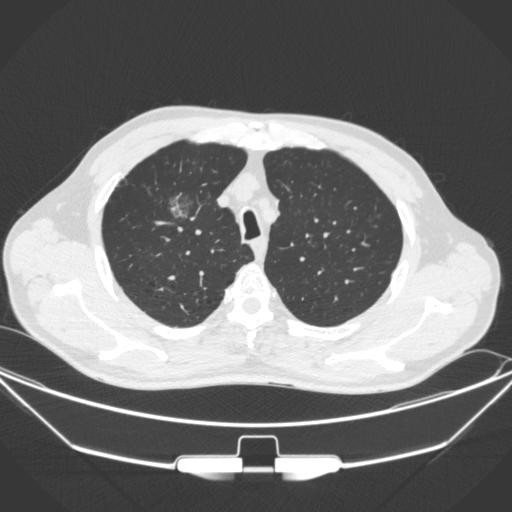
Chest CT, one axial slice. Position 272 of 355 along the scan axis. Lung window (W 1500 / L -600 HU). 1 mm slice thickness. 512 × 512 image matrix, field of view 399 × 399 mm. Patient: male, 67 years. Case-level facts recorded for this patient, not image findings: clinical TNM (as recorded): T1c N0 M0.
Outlined on this slice (rectangle marked by the reading radiologist):
- lung tumour (recorded histology: adenocarcinoma): bounding box <157,188,194,216> (left, top, right, bottom; pixels)